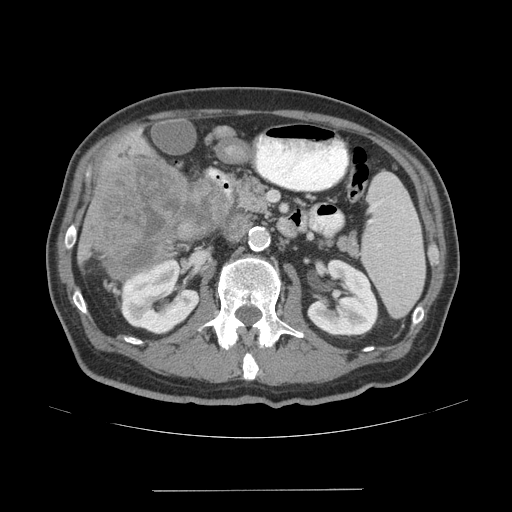
Contrast-enhanced abdominal CT (liver protocol), one axial slice; slice 14 of 77 in the series (ordered by position); reconstruction kernel STANDARD; soft-tissue window (W 400 / L 40 HU); 2.5 mm slice thickness; 512 × 512 image matrix, field of view 400 × 400 mm. Case-level facts recorded for this patient, not image findings: diagnosis: hepatocellular carcinoma (patient treated with transarterial chemoembolisation; whether this scan precedes or follows treatment is not stated here); TNM stage (as recorded): Stage-IVA; Child-Pugh class: A; tumour differentiation: well differentiated.
Outlined on this slice (semi-automatically segmented with operator editing):
- liver parenchyma outside the tumour (the mass and vessels are separate outlines, so this box may not span the whole liver): bounding box <78,132,174,293> (left, top, right, bottom; pixels)
- mass: <92,151,228,278>